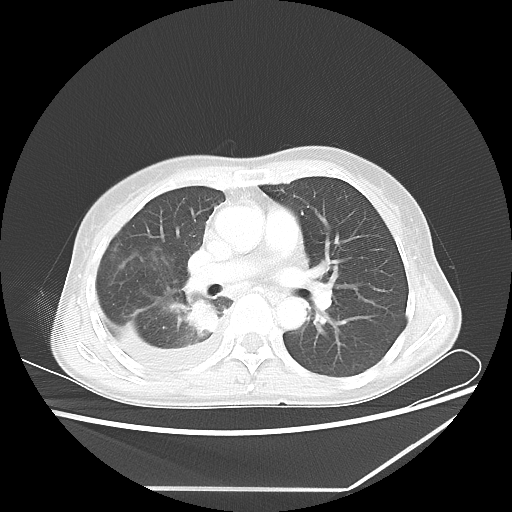
Chest CT, one axial slice; position 34 of 60 along the scan axis; lung window (W 1500 / L -600 HU); 5 mm slice thickness; 512 × 512 image matrix. Female patient, age 59 years. From the clinical record (not read from this slice): clinical TNM (as recorded): T1c N1 M1.
Outlined on this slice (rectangle marked by the reading radiologist):
- lung tumour (recorded histology: adenocarcinoma): bounding box <184,299,219,333> (left, top, right, bottom; pixels)